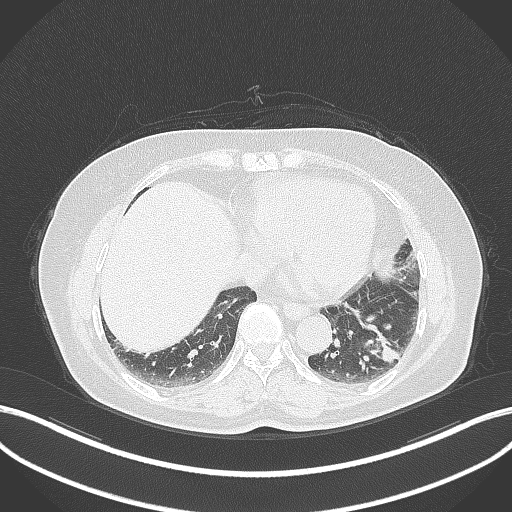
Chest CT, one axial slice; position 118 of 311 along the scan axis; 120 kVp; lung window (W 1500 / L -600 HU); 1 mm slice thickness; 512 × 512 image matrix, field of view 400 × 400 mm. Female patient, age 59 years. From the clinical record (not read from this slice): clinical TNM (as recorded): T2a N0 M0.
Annotated regions visible in this slice (rectangle marked by the reading radiologist):
- lung tumour (recorded histology: adenocarcinoma): bounding box <356,317,403,366> (left, top, right, bottom; pixels)